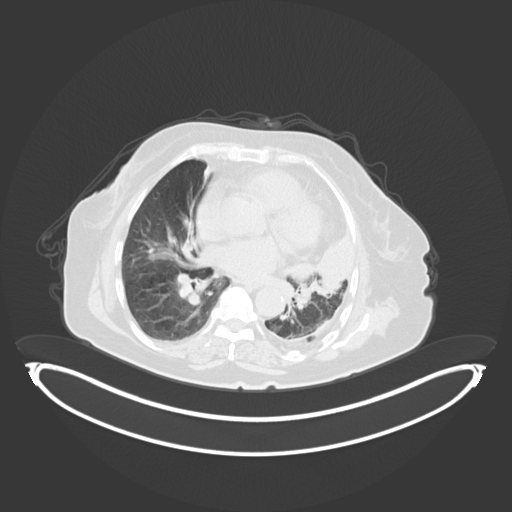
Chest CT, one axial slice. Position 192 of 284 along the scan axis. Lung window (W 1500 / L -600 HU). 3 mm slice thickness. 512 × 512 image matrix, field of view 500 × 500 mm. Patient: female, 75 years. From the clinical record (not read from this slice): clinical TNM (as recorded): T3 N3 M1.
Outlined on this slice (rectangle marked by the reading radiologist):
- lung tumour (recorded histology: adenocarcinoma): bounding box (x1, y1, x2, y2) in pixels: (283, 227, 363, 301)